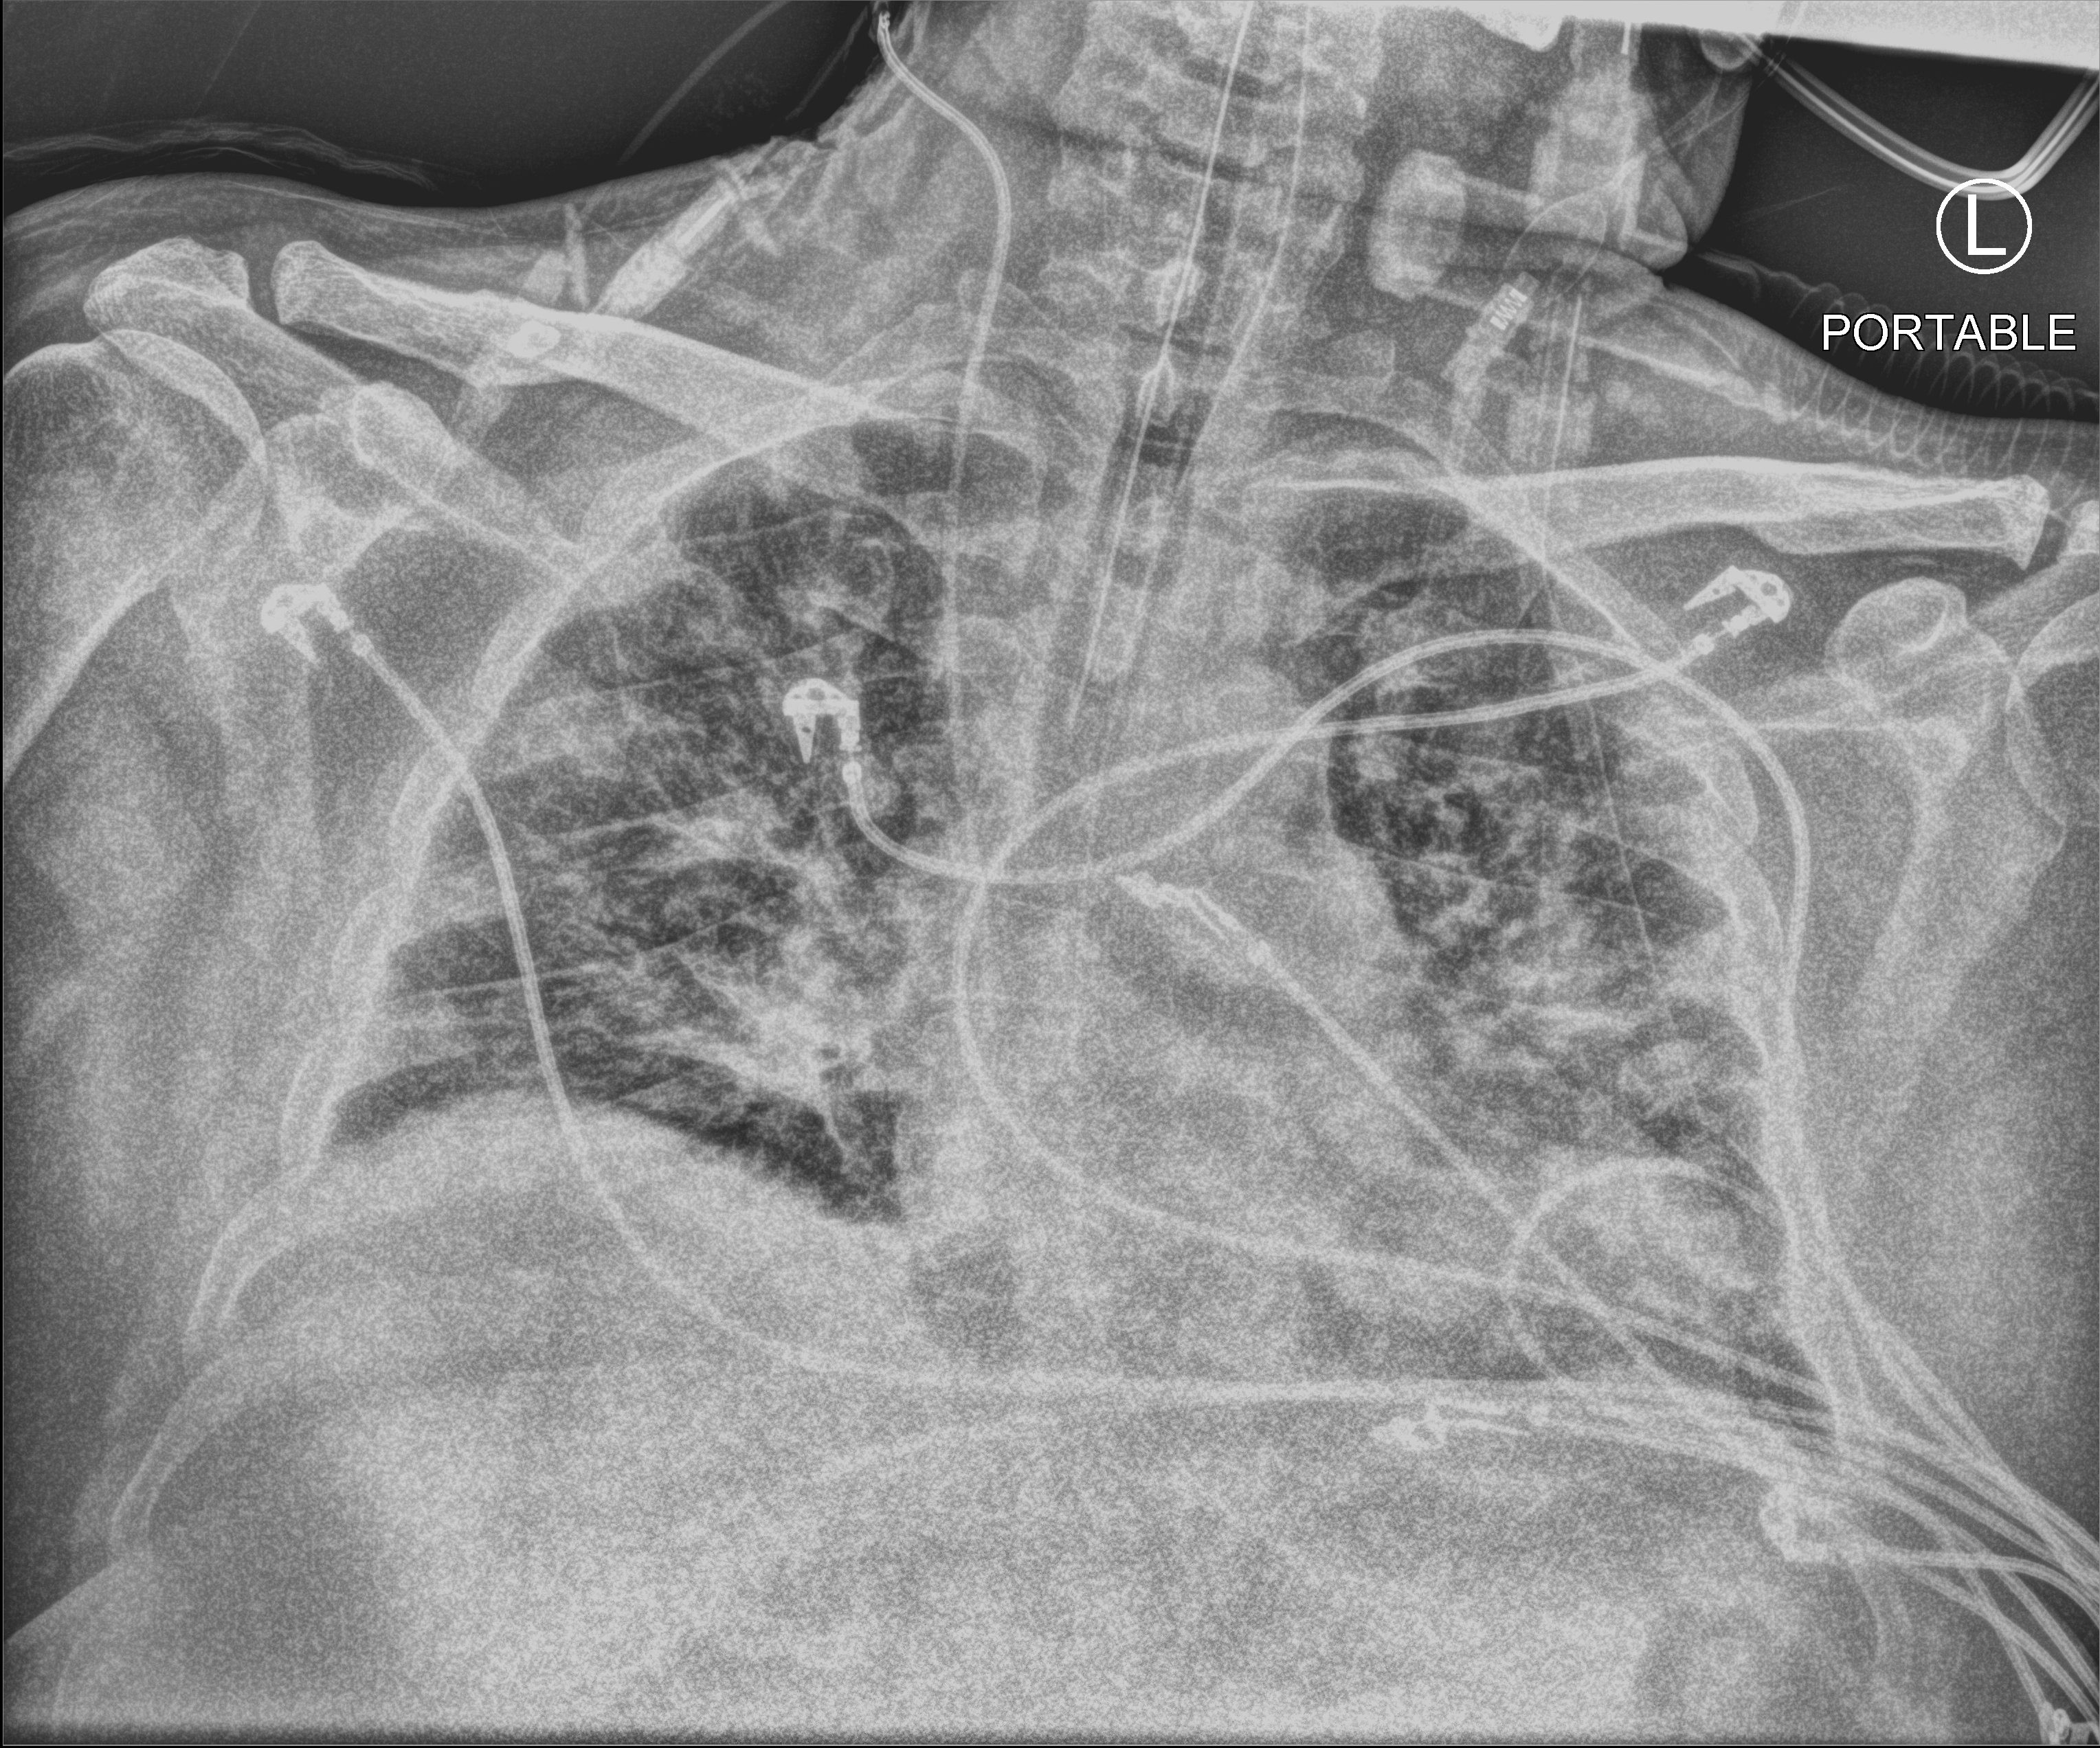
Portable chest radiograph; anteroposterior (AP) projection. Male patient hospitalised with COVID-19, age 18–59 years.
From the hospital-stay record, not from the radiograph (when in the stay this image was taken is not recorded): diabetes (admission record): yes; admitted to intensive care during this hospital stay: yes.